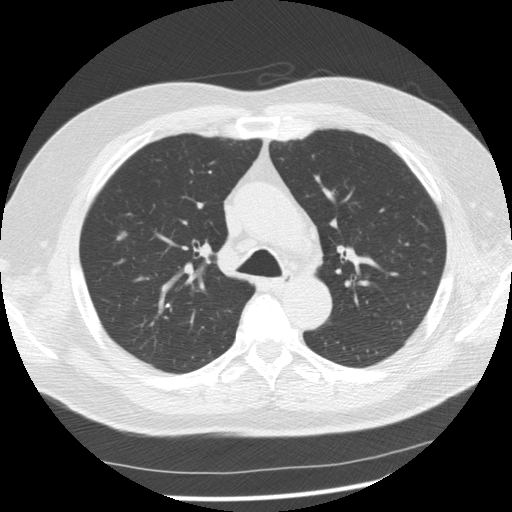
Axial slice from a low-dose chest CT screening exam. Second annual screen. Lung window (W 1500 / L -600 HU). 2.5 mm slice thickness. Slice 38 of 136 in the series. Male participant, aged 61 years at enrolment.
Expert-annotated lung lesion, bounding box <104,224,135,252> (left, top, right, bottom; pixels). Reader record for this screening exam (exam-level; its link to the box is not recorded): non-calcified nodule or mass ≥4 mm, right upper lobe, 7 × 7 mm, smooth margins, soft tissue attenuation, pre-existing on the prior screen: yes; interval growth: no. Later outcome: lung cancer diagnosed 389 days after this screen (after the third annual screen) — adenocarcinoma, NOS, right upper lobe, stage IIIA (AJCC 6th edition), 13 mm at pathology.